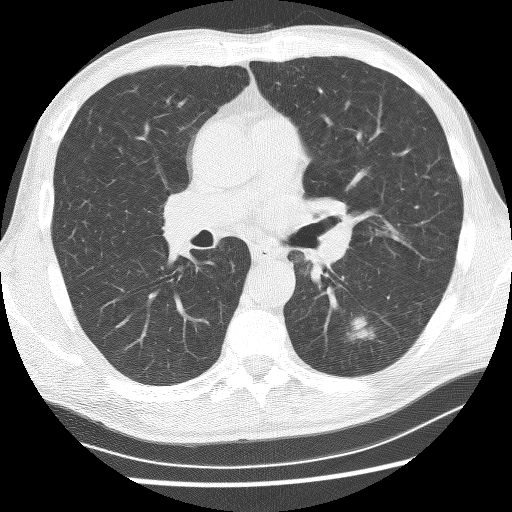
Low-dose screening chest CT, one axial slice. Position 140 of 253 along the scan axis. Reconstruction kernel BONE. 120 kVp. Lung window (W 1500 / L -600 HU). 512 × 512 image matrix, field of view 340 × 340 mm.
Outlined on this slice (expert manual segmentation):
- lesion 1 (tumor, lower lobe of left lung): bounding box [x1, y1, x2, y2] px = [349, 317, 374, 340]